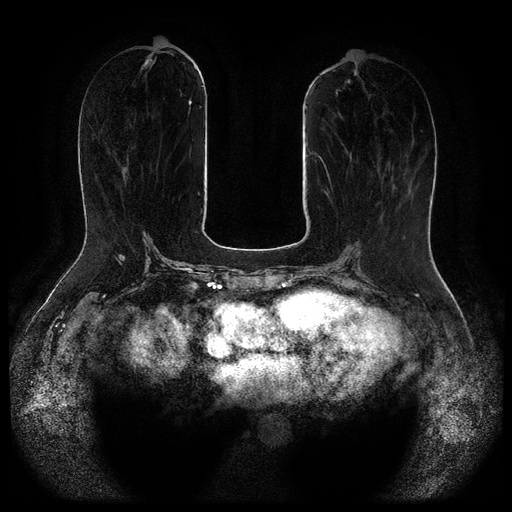
Breast MRI (dynamic contrast-enhanced, multi-phase), one axial slice. Position 38 of 116 along the scan axis. Dynamic contrast-enhanced series, time point 2 of 5 at this slice position (early post-contrast). 1.5 T. TE 2.6 ms, TR 5.3 ms. 2.1 mm slice thickness. 512 × 512 image matrix, field of view 360 × 360 mm. Female patient, age 65 years.
Outlined on this slice (semi-automatic segmentation, software-assisted and operator-edited):
- breast lesion (labelled 'tumour' in the annotation; benign lesions carry a separate 'benign' label): box from (x=145, y=56) to (x=152, y=66) px